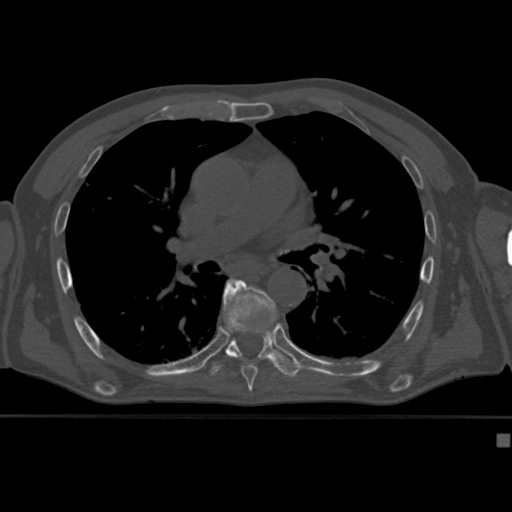
CT including the spine, one axial slice; reconstruction kernel Br40s; bone window (W 1800 / L 400 HU); 512 × 512 image matrix, field of view 337 × 337 mm. Patient: male, 64 years. From the clinical record (not read from this slice): primary cancer: uterus; vertebrae with lytic lesions (as recorded): T1, T4, T5, T7, L5.
Annotated regions visible in this slice (semi-automatic segmentation, software-assisted and operator-edited):
- T7 vertebra: box from (x=223, y=278) to (x=276, y=382) px
- T8 vertebra: (x=209, y=277)–(x=300, y=378)